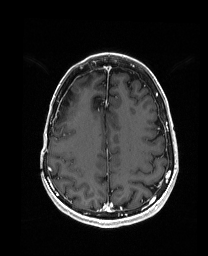
Brain MRI from a brain-tumour surgery series, one axial slice; slice 58 of 192 in the series (ordered by position); T1-weighted post-contrast; 1 mm slice thickness; 208 × 256 image matrix. Case-level facts recorded for this patient, not image findings: histopathology: Metastatic Carcinoma from Breast primary; tumour location: Right Frontal.
Outlined on this slice (expert manual segmentation):
- previous resection cavity: bounding box <62,87,73,106> (left, top, right, bottom; pixels)